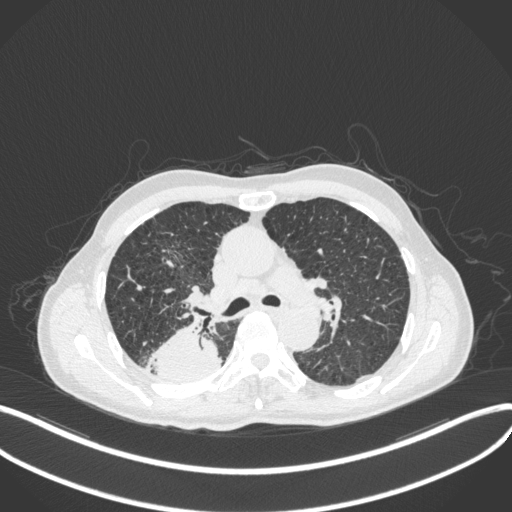
Chest CT, one axial slice. Slice 292 of 423 in the series (ordered by position). 120 kVp. Lung window (W 1500 / L -600 HU). 512 × 512 image matrix, field of view 400 × 400 mm. Male patient, age 79 years. Case-level facts recorded for this patient, not image findings: clinical TNM (as recorded): T3 N0 M0.
Annotated regions visible in this slice (bounding box drawn by a radiologist):
- lung tumour (recorded histology: adenocarcinoma): bounding box (x1, y1, x2, y2) in pixels: (146, 320, 225, 384)